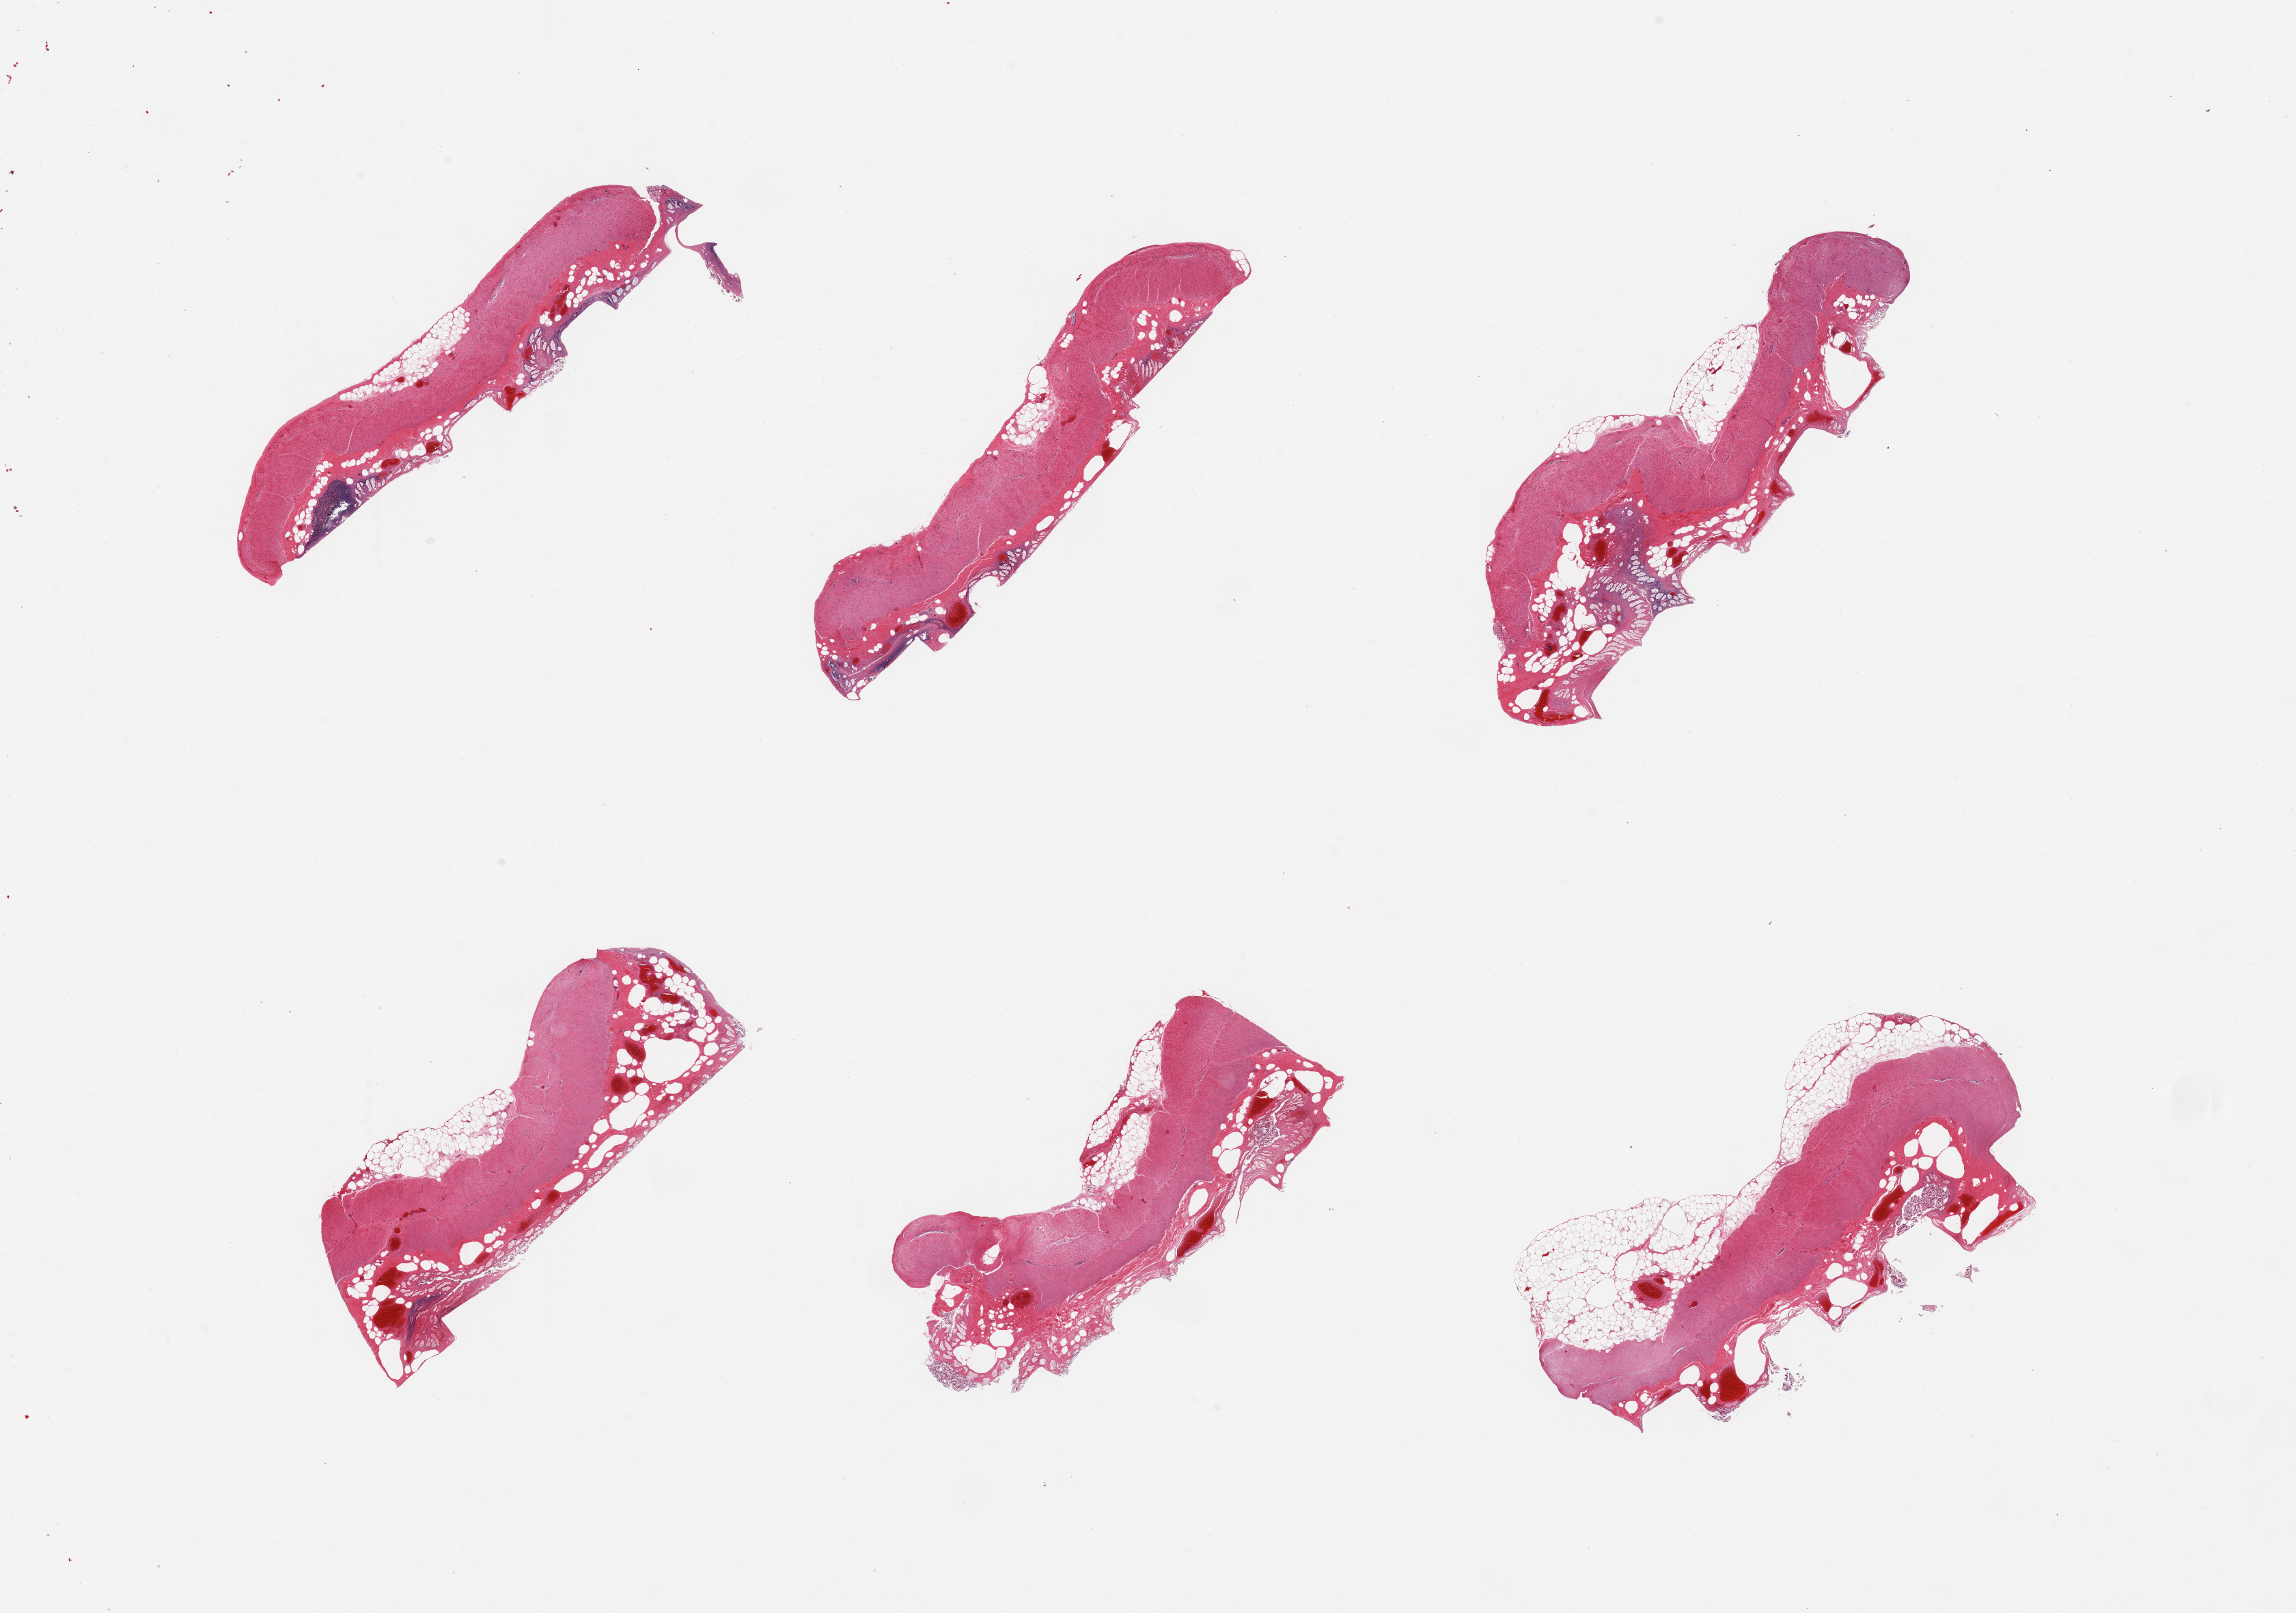
Digitized hematoxylin and eosin (H&E)-stained section — a low-resolution overview of the entire scanned area, about 26.6 x 18.7 mm (from a 20x scan). PAXgene-fixed paraffin-embedded (PFPE) section. Sampled site (target tissue): transverse colon. Tissue donor sample.
Reviewer comment on this tissue sample: 6 pieces; mucosa largely autolyzed; inner muscle moderately autolyzed.